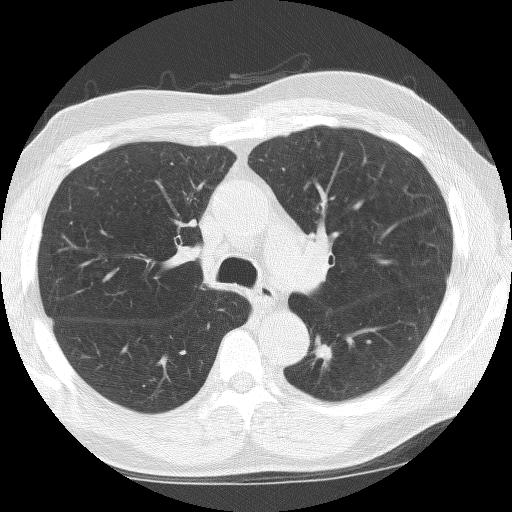
Chest CT (low-dose screening protocol), one axial image; baseline screening round; lung window (W 1500 / L -600 HU); 2.5 mm slice thickness; slice 58 of 155 in the series. Male participant, aged 67 years at enrolment. Current smoker at enrolment.
- Expert reader's lesion annotation, bounding box <297,335,342,388> (left, top, right, bottom; pixels).
- Reader record for this screening exam (exam-level; its link to the box is not recorded): non-calcified nodule or mass ≥4 mm, left lower lobe, 18 × 13 mm, spiculated (stellate) margins, soft tissue attenuation.
- Official screen result: positive, change unspecified: nodule(s) >= 4 mm or enlarging nodule(s), mass(es), or other non-specific abnormalities suspicious for lung cancer.
- Participant outcome: lung cancer diagnosed 5 days after this screen — non-small cell carcinoma, left lower lobe, undifferentiated (G4), stage IA (AJCC 6th edition), 12 mm at pathology.